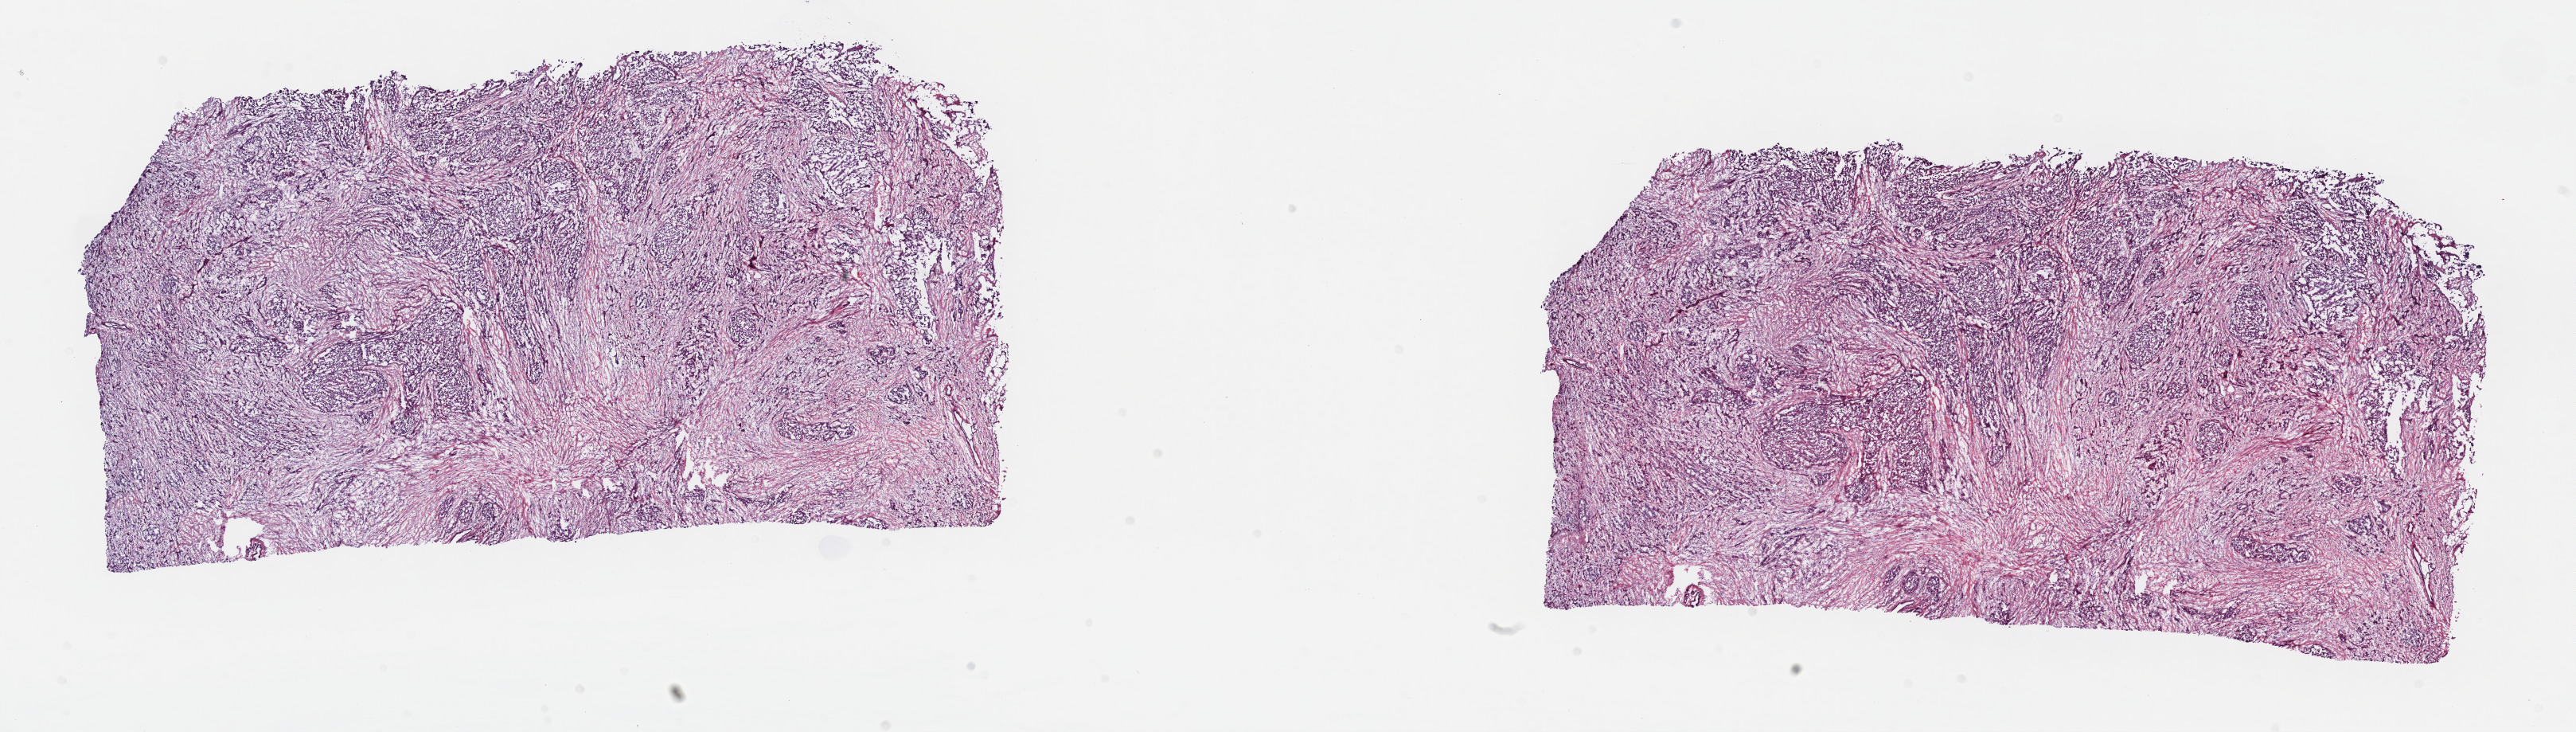
Digitized H&E tissue section (whole slide) — whole scanned area (about 26.2 x 7.4 mm) shown as a low-resolution overview. Frozen section. Pancreas, primary tumour sample. Male patient; age at initial diagnosis 49 years. Histologic grade: G2 (moderately differentiated). Slide review estimates, as recorded: tumour cells 100%, tumour nuclei 65%, normal cells 0%, stromal cells 0%, necrosis 0%. Infiltration values recorded for this section: lymphocyte infiltration 3%, monocyte infiltration 0%, neutrophil infiltration 0%.
* diagnosis: Infiltrating duct carcinoma, NOS (head of pancreas)
* lymph nodes positive (case pathology): 3 of 27 examined
* AJCC pathologic stage: IIB